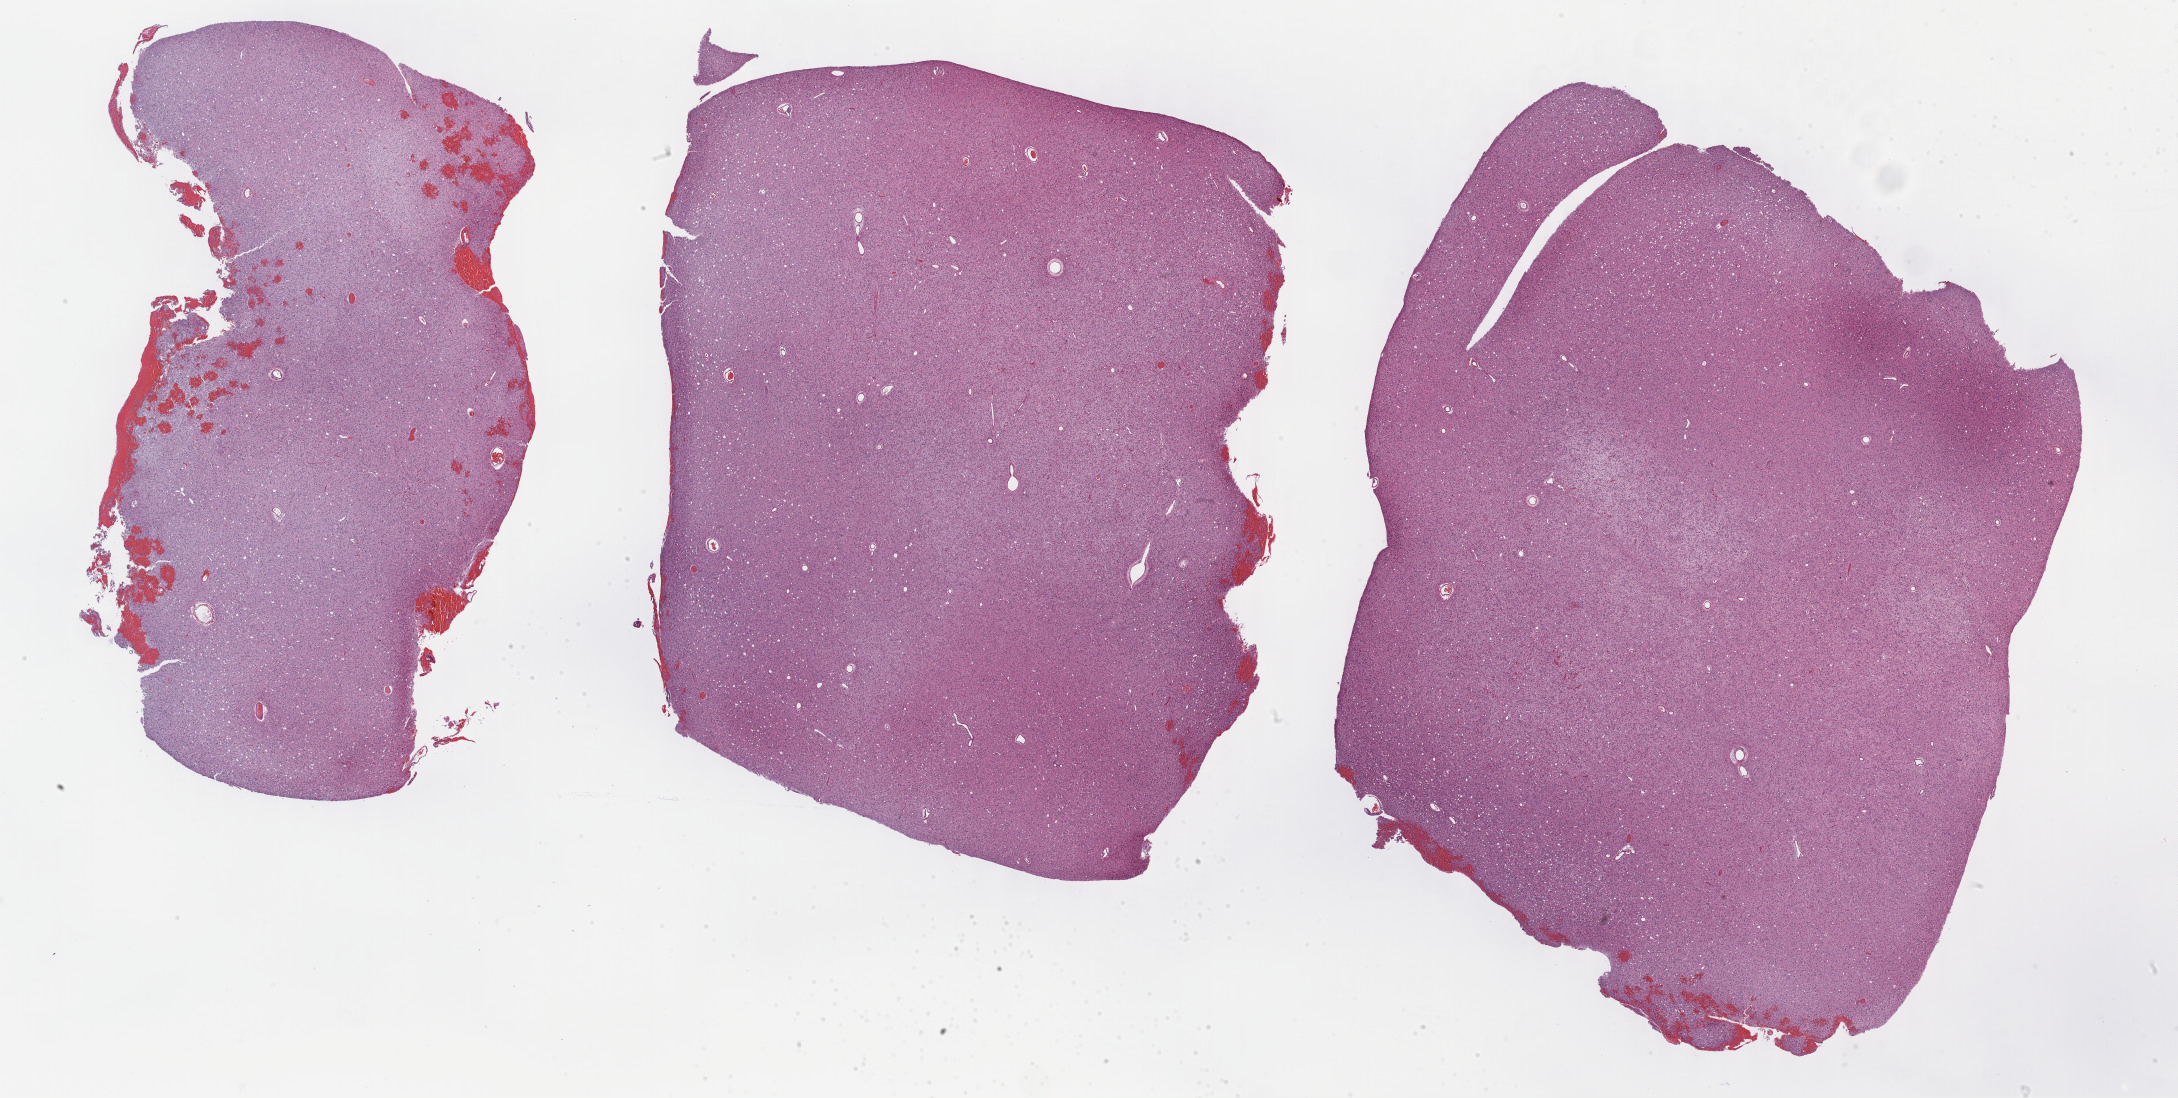
Digitized H&E tissue section (whole slide), a low-resolution overview of the entire scanned area, about 35.2 x 17.8 mm; formalin-fixed paraffin-embedded (FFPE) diagnostic section; primary tumour sample from the brain. Female patient; age at initial diagnosis 24 years. Histologic grade: G2 (moderately differentiated).
Laterality: right. Pathologic diagnosis: Astrocytoma, NOS (cerebrum).